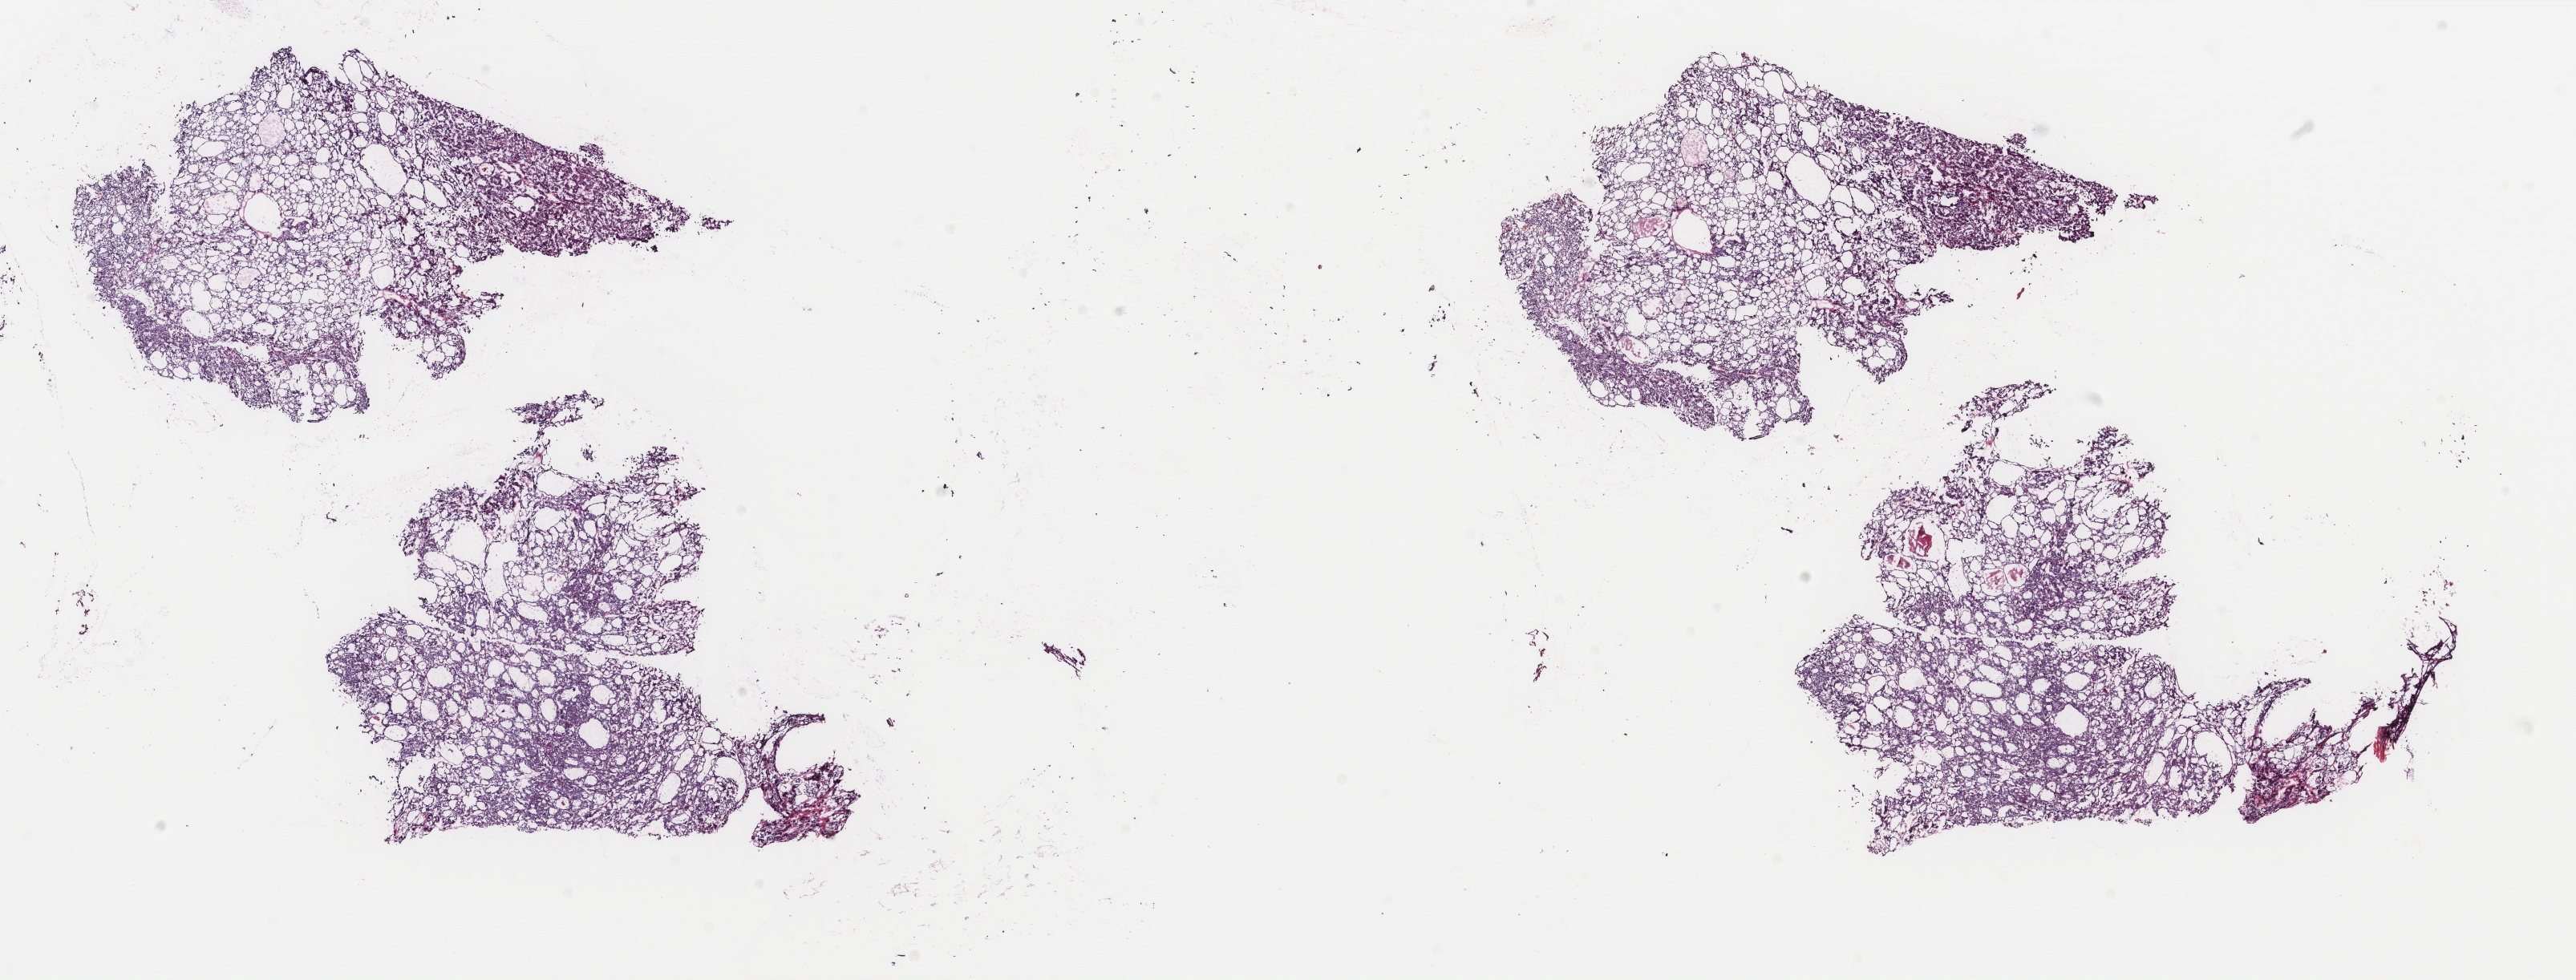
Digitized H&E-stained tissue section (whole slide) — whole scanned area (about 25.5 x 9.7 mm) shown as a low-resolution overview; frozen section from the top of the tissue portion; thyroid, primary tumour sample. Female patient; age at initial diagnosis 30 years. Pathologist review of this section (percent, as recorded): tumour cells 85%, tumour nuclei 85%, normal cells 0%, stromal cells 15%, necrosis 0%. Inflammatory infiltration, as recorded: lymphocyte infiltration 1%, monocyte infiltration 0%, neutrophil infiltration 0%.
* AJCC pathologic stage: I (7th edition)
* laterality: bilateral
* TNM: T3 N0 M0
* diagnosis: Papillary adenocarcinoma, NOS (thyroid gland)